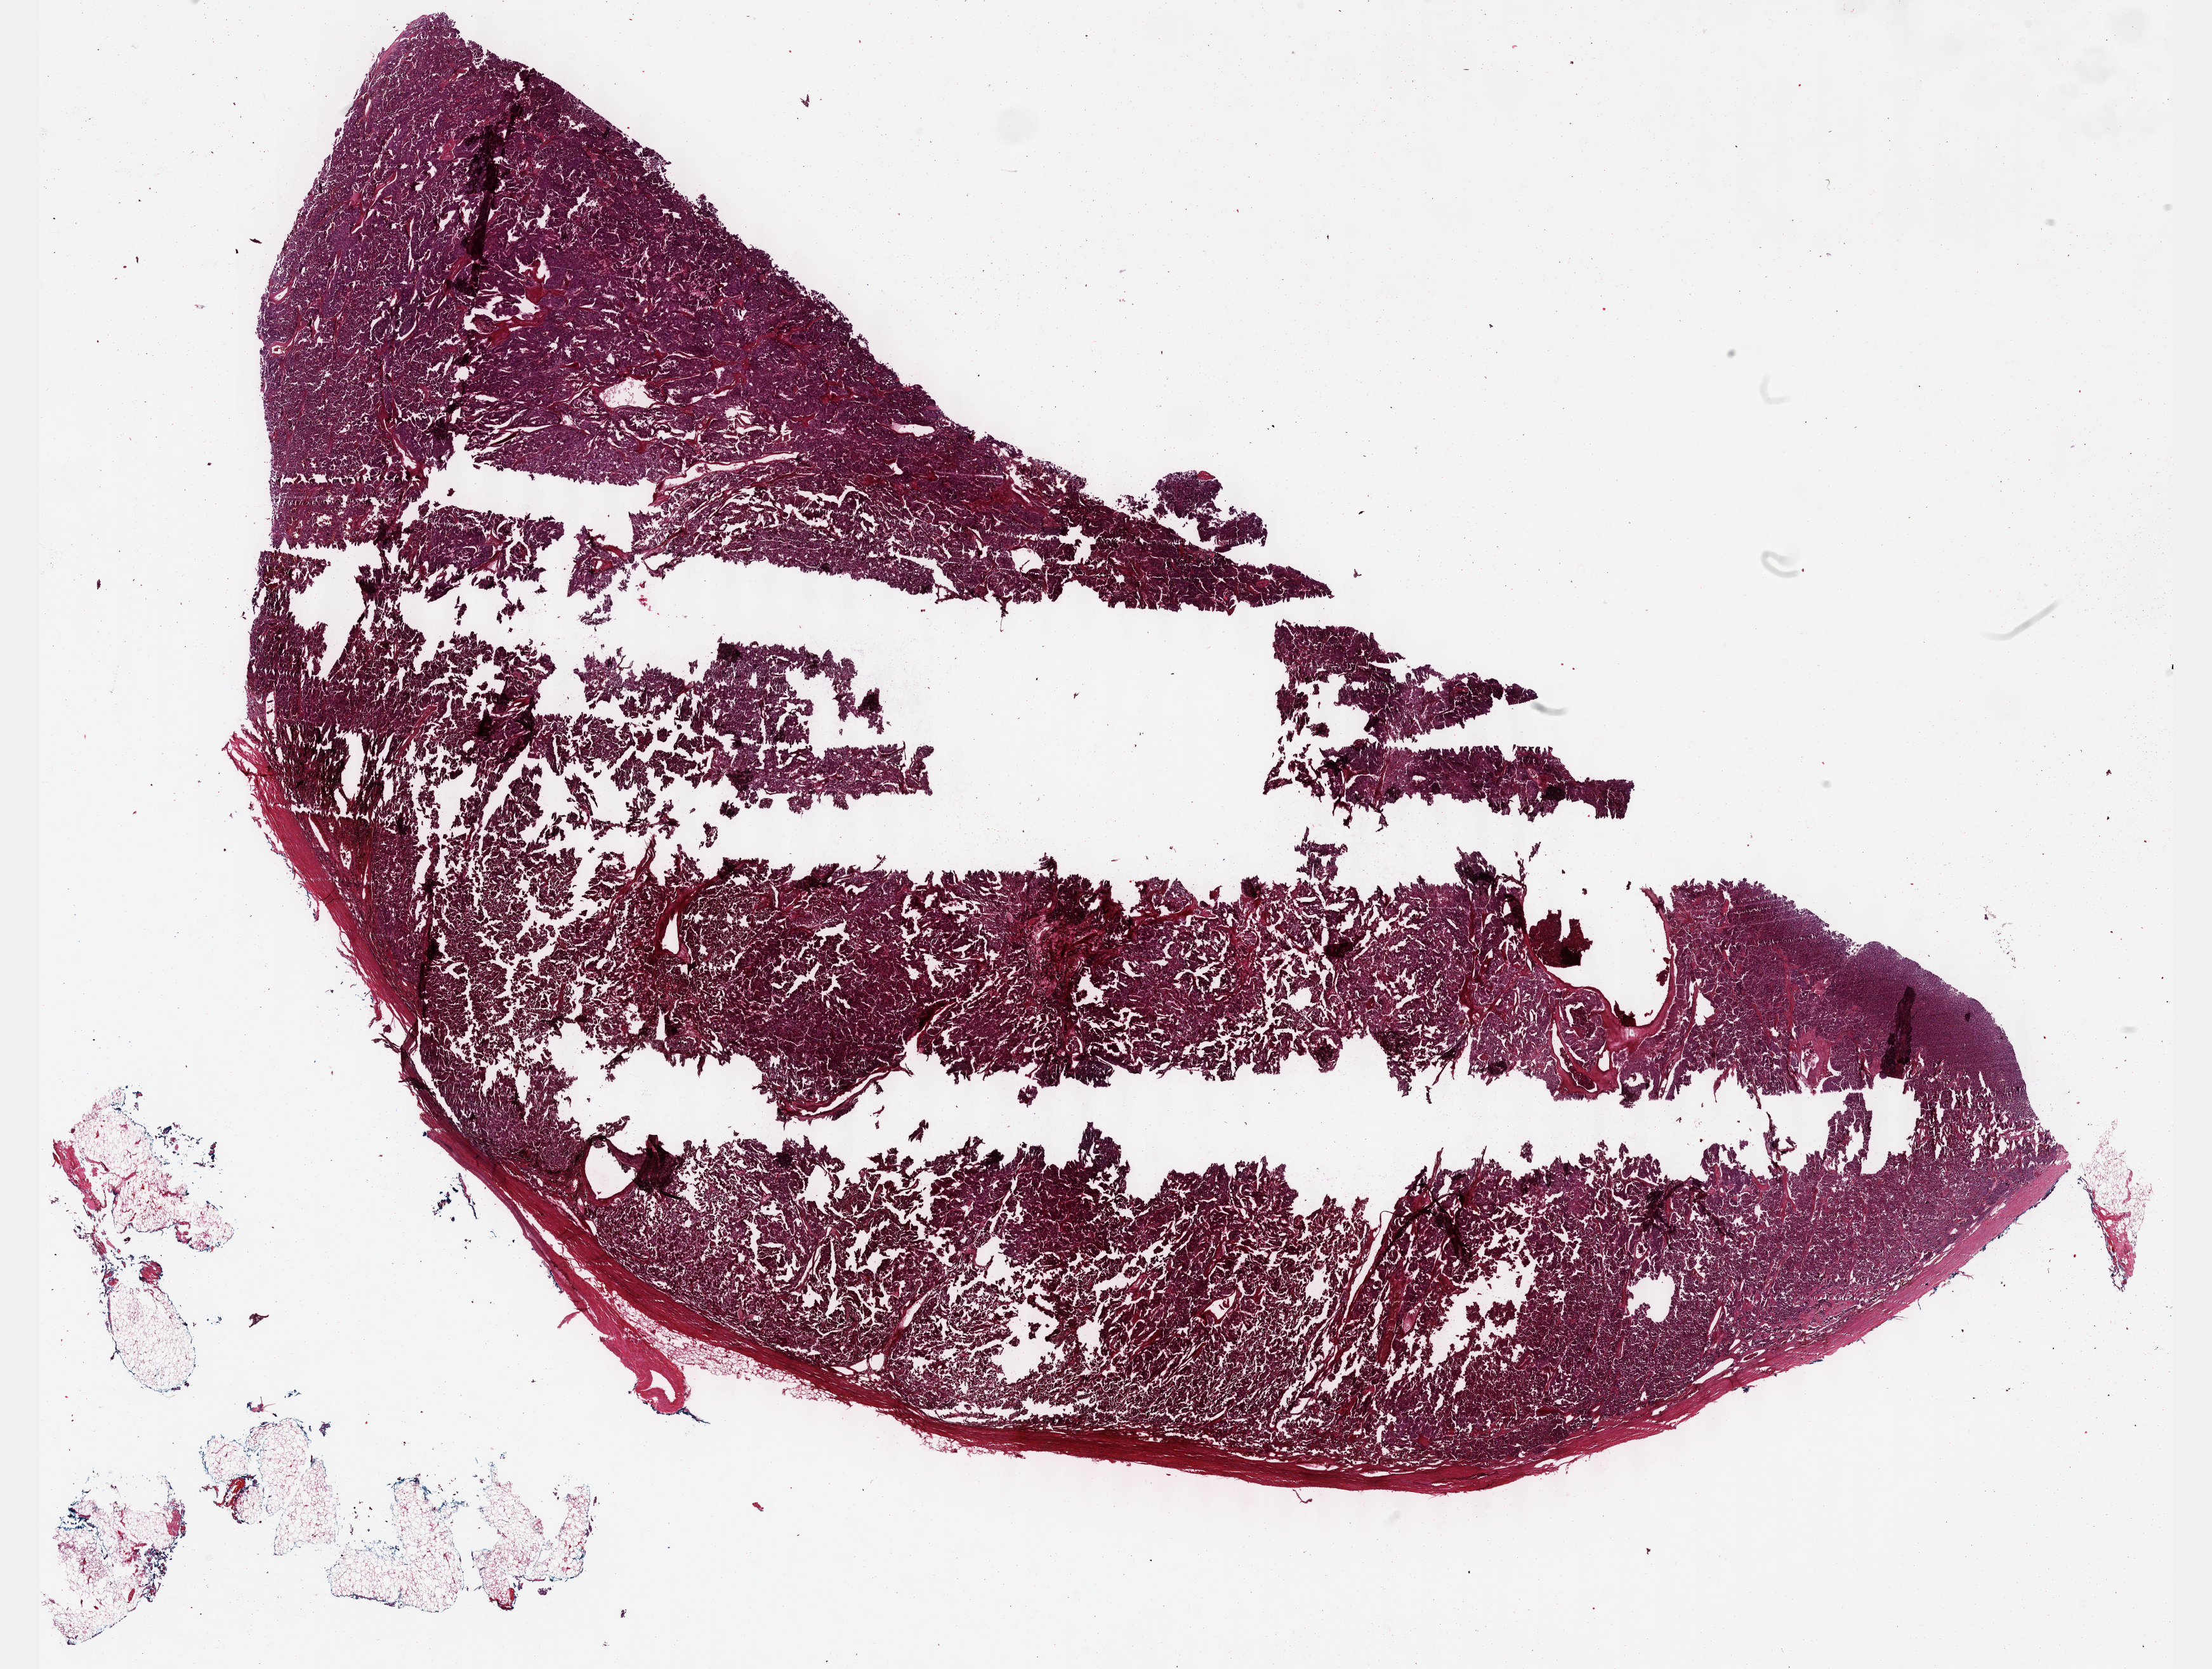
Digitized Hematoxylin and eosin (H&E) stained tissue section (whole slide), shown as a low-resolution overview of the whole scanned area (about 28.2 x 21.3 mm), formalin-fixed paraffin-embedded (FFPE) diagnostic section, adrenal gland, primary tumour sample. Male patient; age at initial diagnosis 40 years.
Pathologic diagnosis: Pheochromocytoma, NOS.